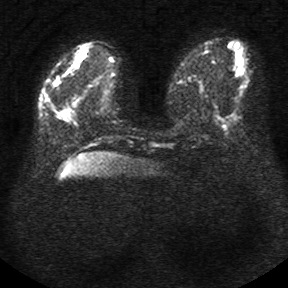
Breast MRI, one axial slice. Position 9 of 34 along the scan axis. Diffusion-weighted series; image 2 of 4 stored at this slice position (different b-values; order by instance number). 1.5 T. 5 mm slice thickness. 288 × 288 image matrix. Female patient.
Structures marked on this image (expert manual segmentation):
- tumour on diffusion-weighted imaging: box from (x=62, y=46) to (x=88, y=77) px